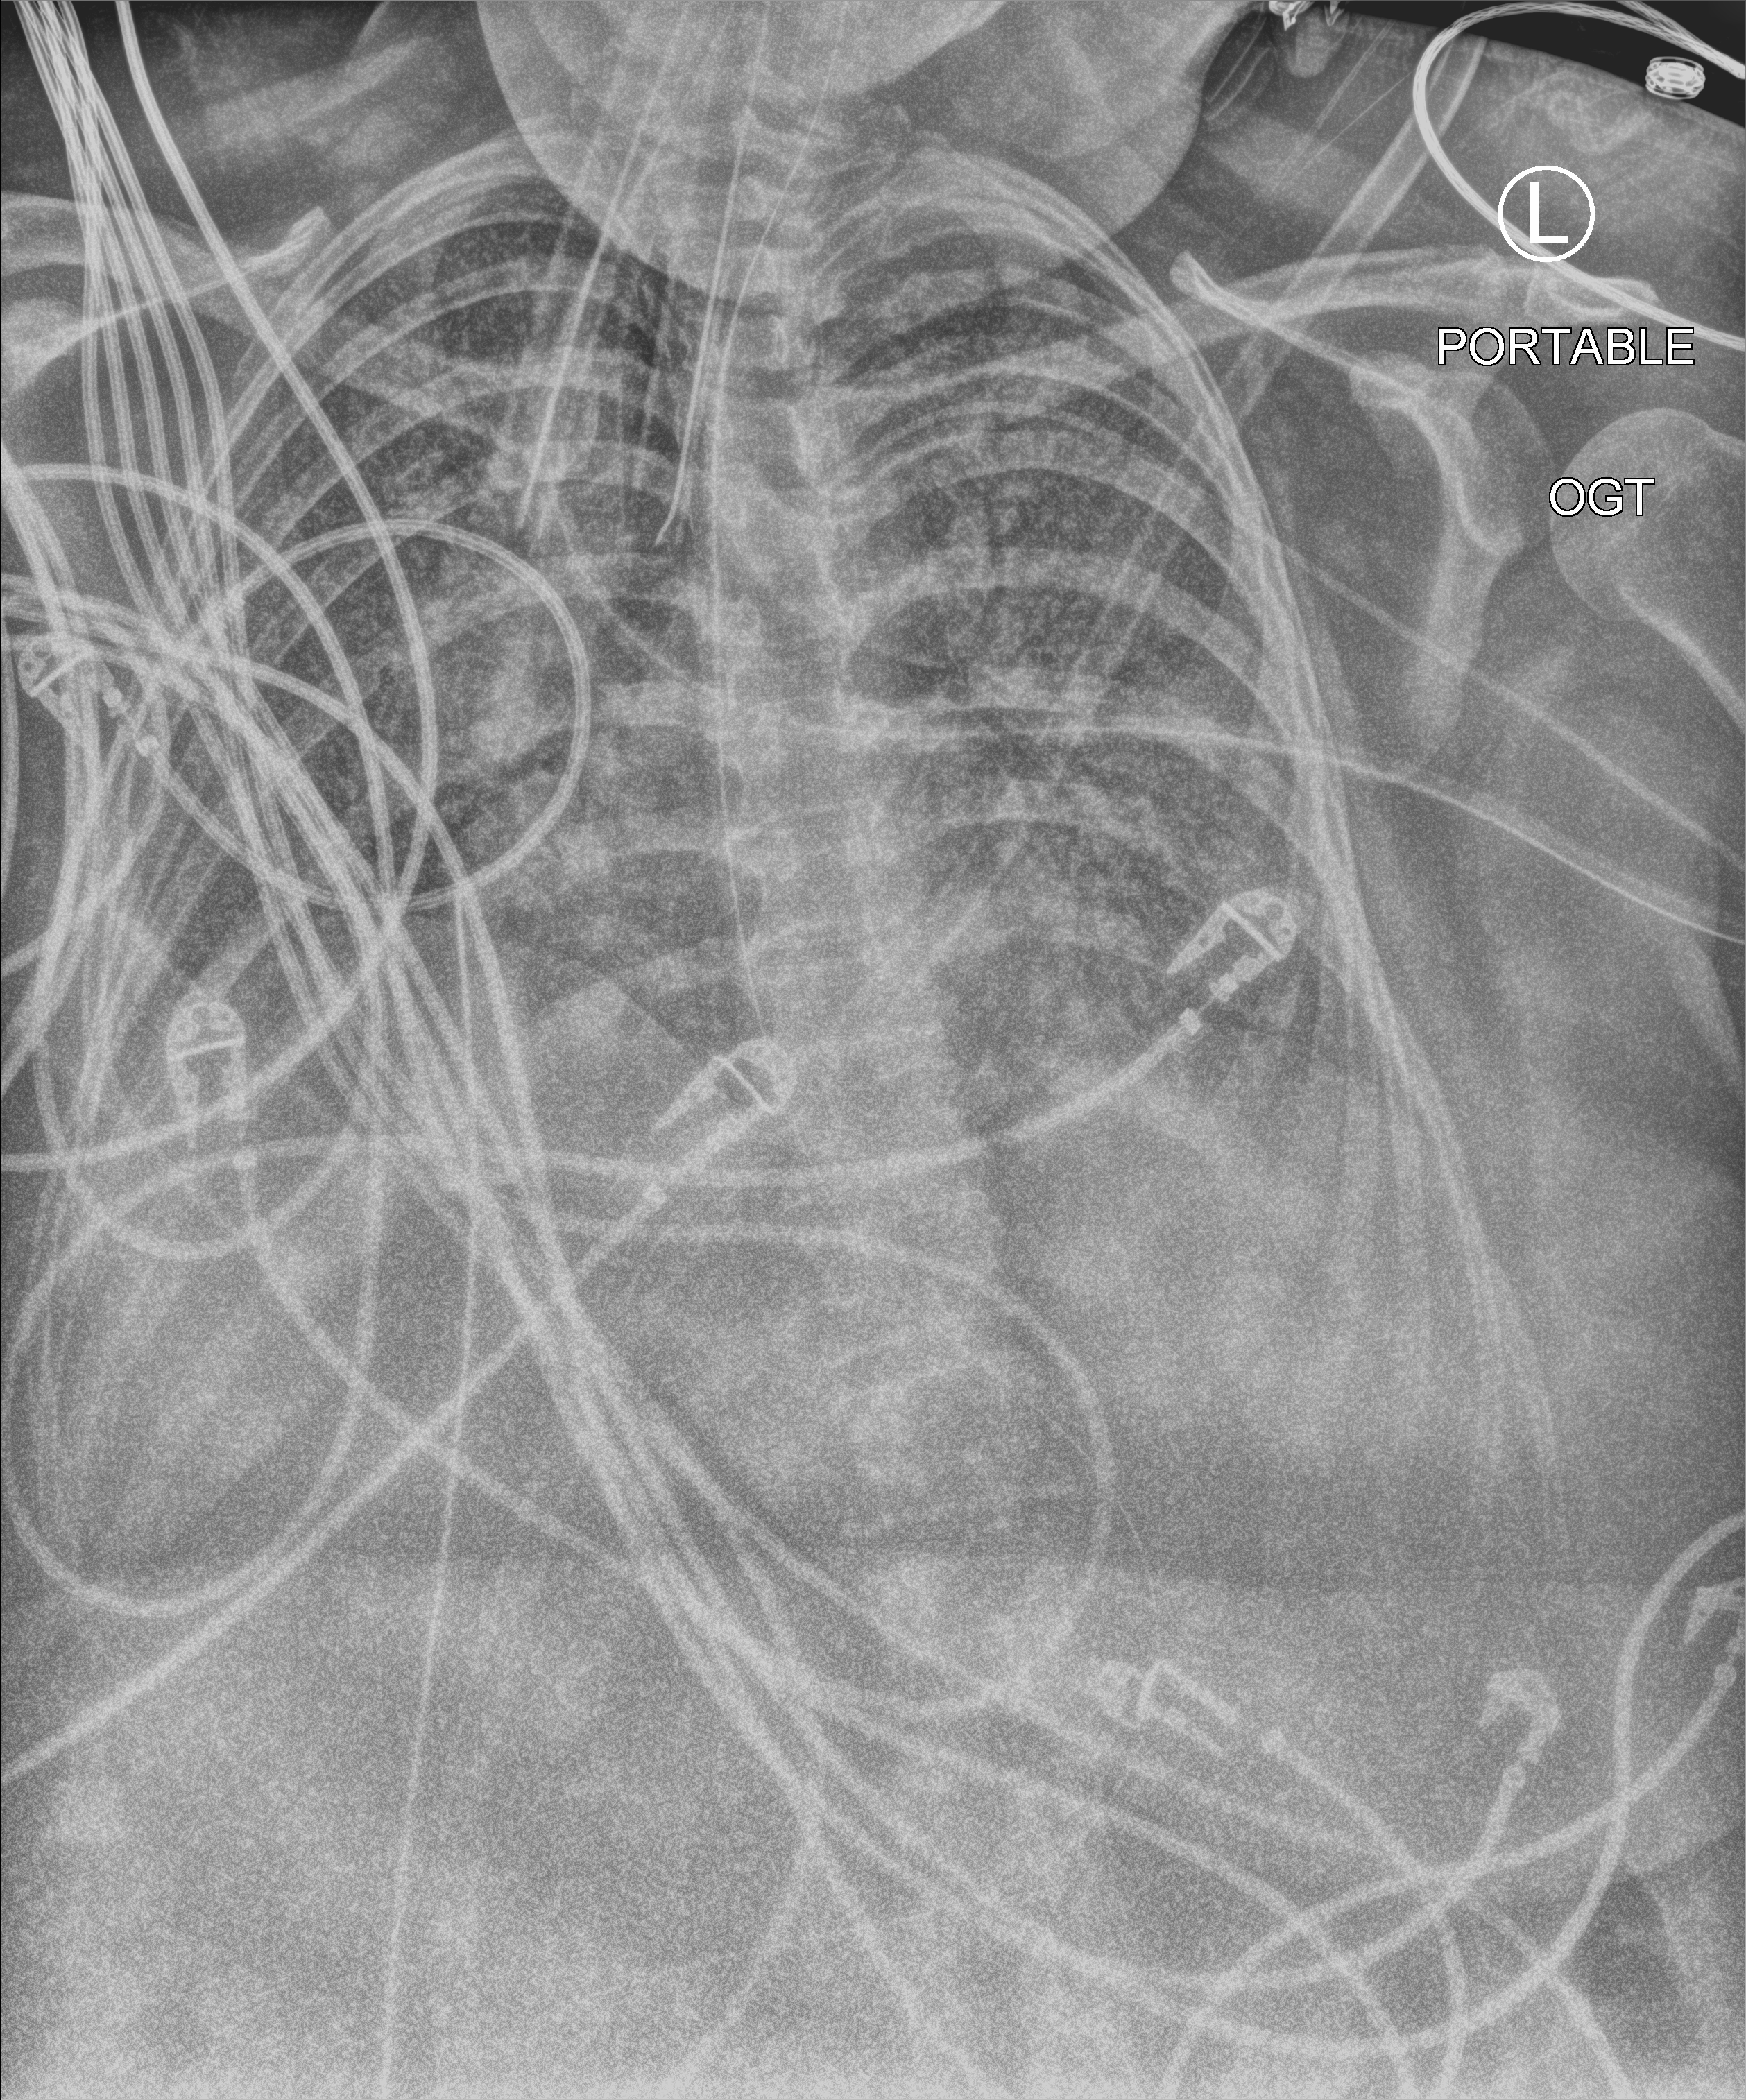
Portable chest radiograph; anteroposterior (AP) projection. Patient hospitalised with COVID-19; female, aged 18–59 years.
From the hospital-stay record, not from the radiograph (when in the stay this image was taken is not recorded):
- COPD (admission record): no
- admitted to intensive care during this hospital stay: yes